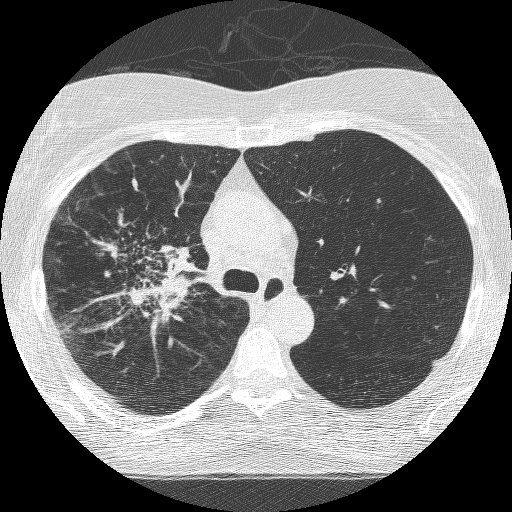
Chest CT (low-dose screening protocol), one axial image, third screening round (two years after baseline), lung window (W 1500 / L -600 HU), 1.25 mm slice thickness, lung (sharp) reconstruction kernel (BONE), 512 × 512 image matrix, field of view 294 × 294 mm. Female participant, aged 64 years at enrolment.
Lesion marked by an expert reader, bounding box (x1, y1, x2, y2) in pixels: (93, 226, 206, 339). Screening reader's record for this exam (one nodule recorded; not confirmed to be the boxed lesion): non-calcified nodule or mass ≥4 mm, right upper lobe, 49 × 43 mm, spiculated (stellate) margins, soft tissue attenuation, pre-existing on the prior screen: yes; interval growth: yes. Official screen result: positive, other. Participant outcome: lung cancer diagnosed 7 days after this screen — adenocarcinoma, NOS, right upper lobe, right middle lobe, right hilum, stage IV (AJCC 6th edition), 85 mm at pathology.